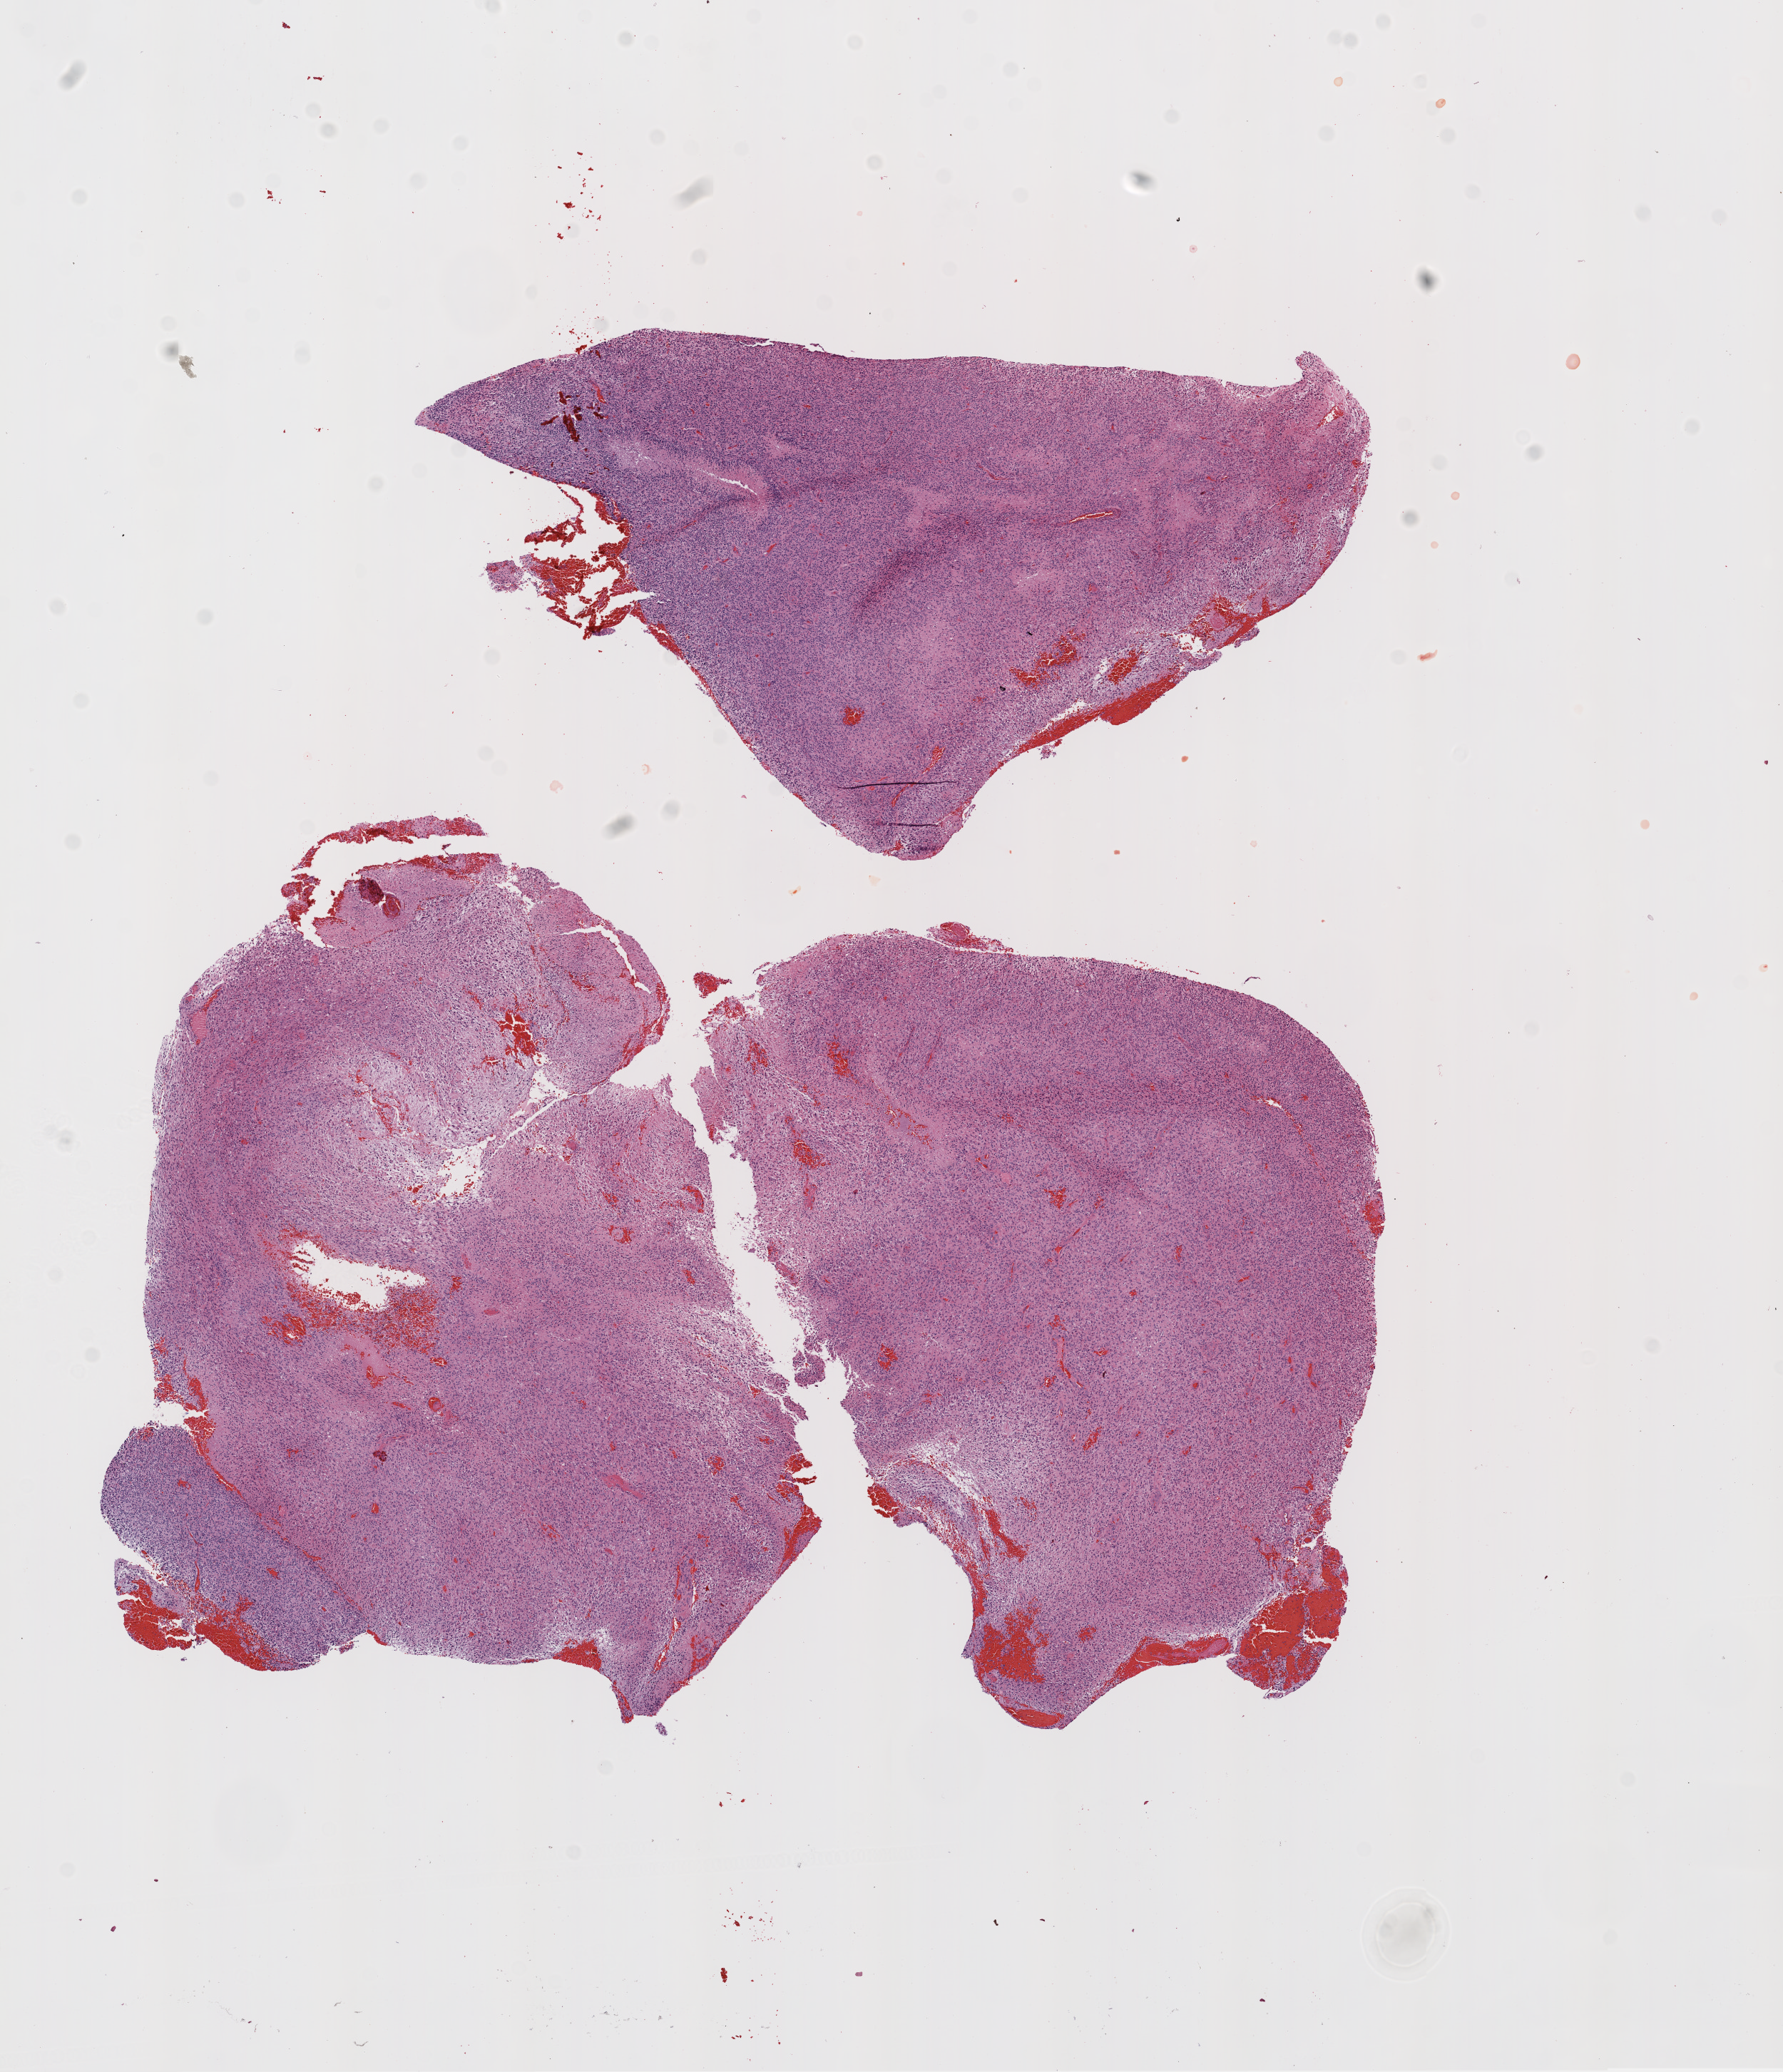
Digitized H&E-stained tissue section (whole slide) — whole scanned area (about 10.0 x 11.7 mm, slide scanned at 20x) shown as a low-resolution overview. Formalin-fixed paraffin-embedded (FFPE) diagnostic section. Primary tumour sample from the brain. Male, age 58 years at initial diagnosis.
Pathologic diagnosis: Glioblastoma.